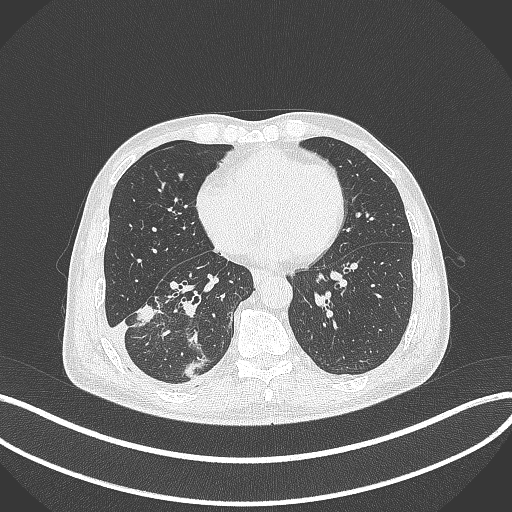
Chest CT, one axial slice. Position 146 of 388 along the scan axis. 120 kVp. Lung window (W 1500 / L -600 HU). 512 × 512 image matrix, field of view 400 × 400 mm. Male patient, age 64 years. Case-level facts recorded for this patient, not image findings: clinical TNM (as recorded): T3 N0 M0.
Structures marked on this image (bounding box drawn by a radiologist):
- lung tumour (recorded histology: adenocarcinoma): bounding box [x1, y1, x2, y2] px = [129, 299, 156, 329]